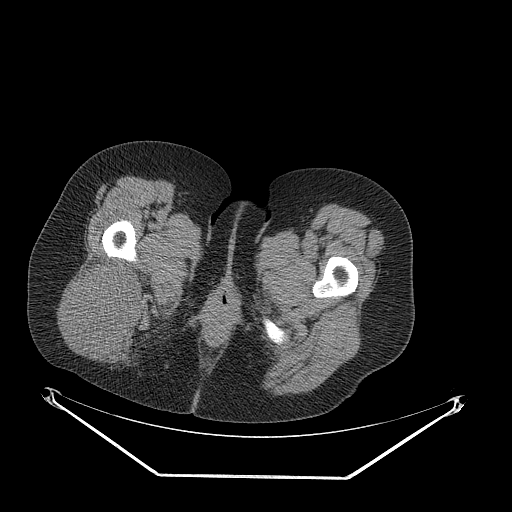
CT of an extremity soft-tissue mass (from a PET/CT study), one axial slice. Position 51 of 257 along the scan axis. 140 kVp. Soft-tissue window (W 400 / L 40 HU). 3.75 mm slice thickness. 512 × 512 image matrix, field of view 500 × 500 mm. Female patient. From the clinical record (not read from this slice): histological type: synovial sarcoma; grade: intermediate; site of the primary tumour: right buttock.
Annotated regions visible in this slice (expert contour drawn on MRI and transferred to this co-registered scan by the dataset authors):
- gross tumour volume including surrounding oedema: box from (x=69, y=256) to (x=145, y=352) px
- gross tumour volume (mass): (x=69, y=256)–(x=145, y=352)